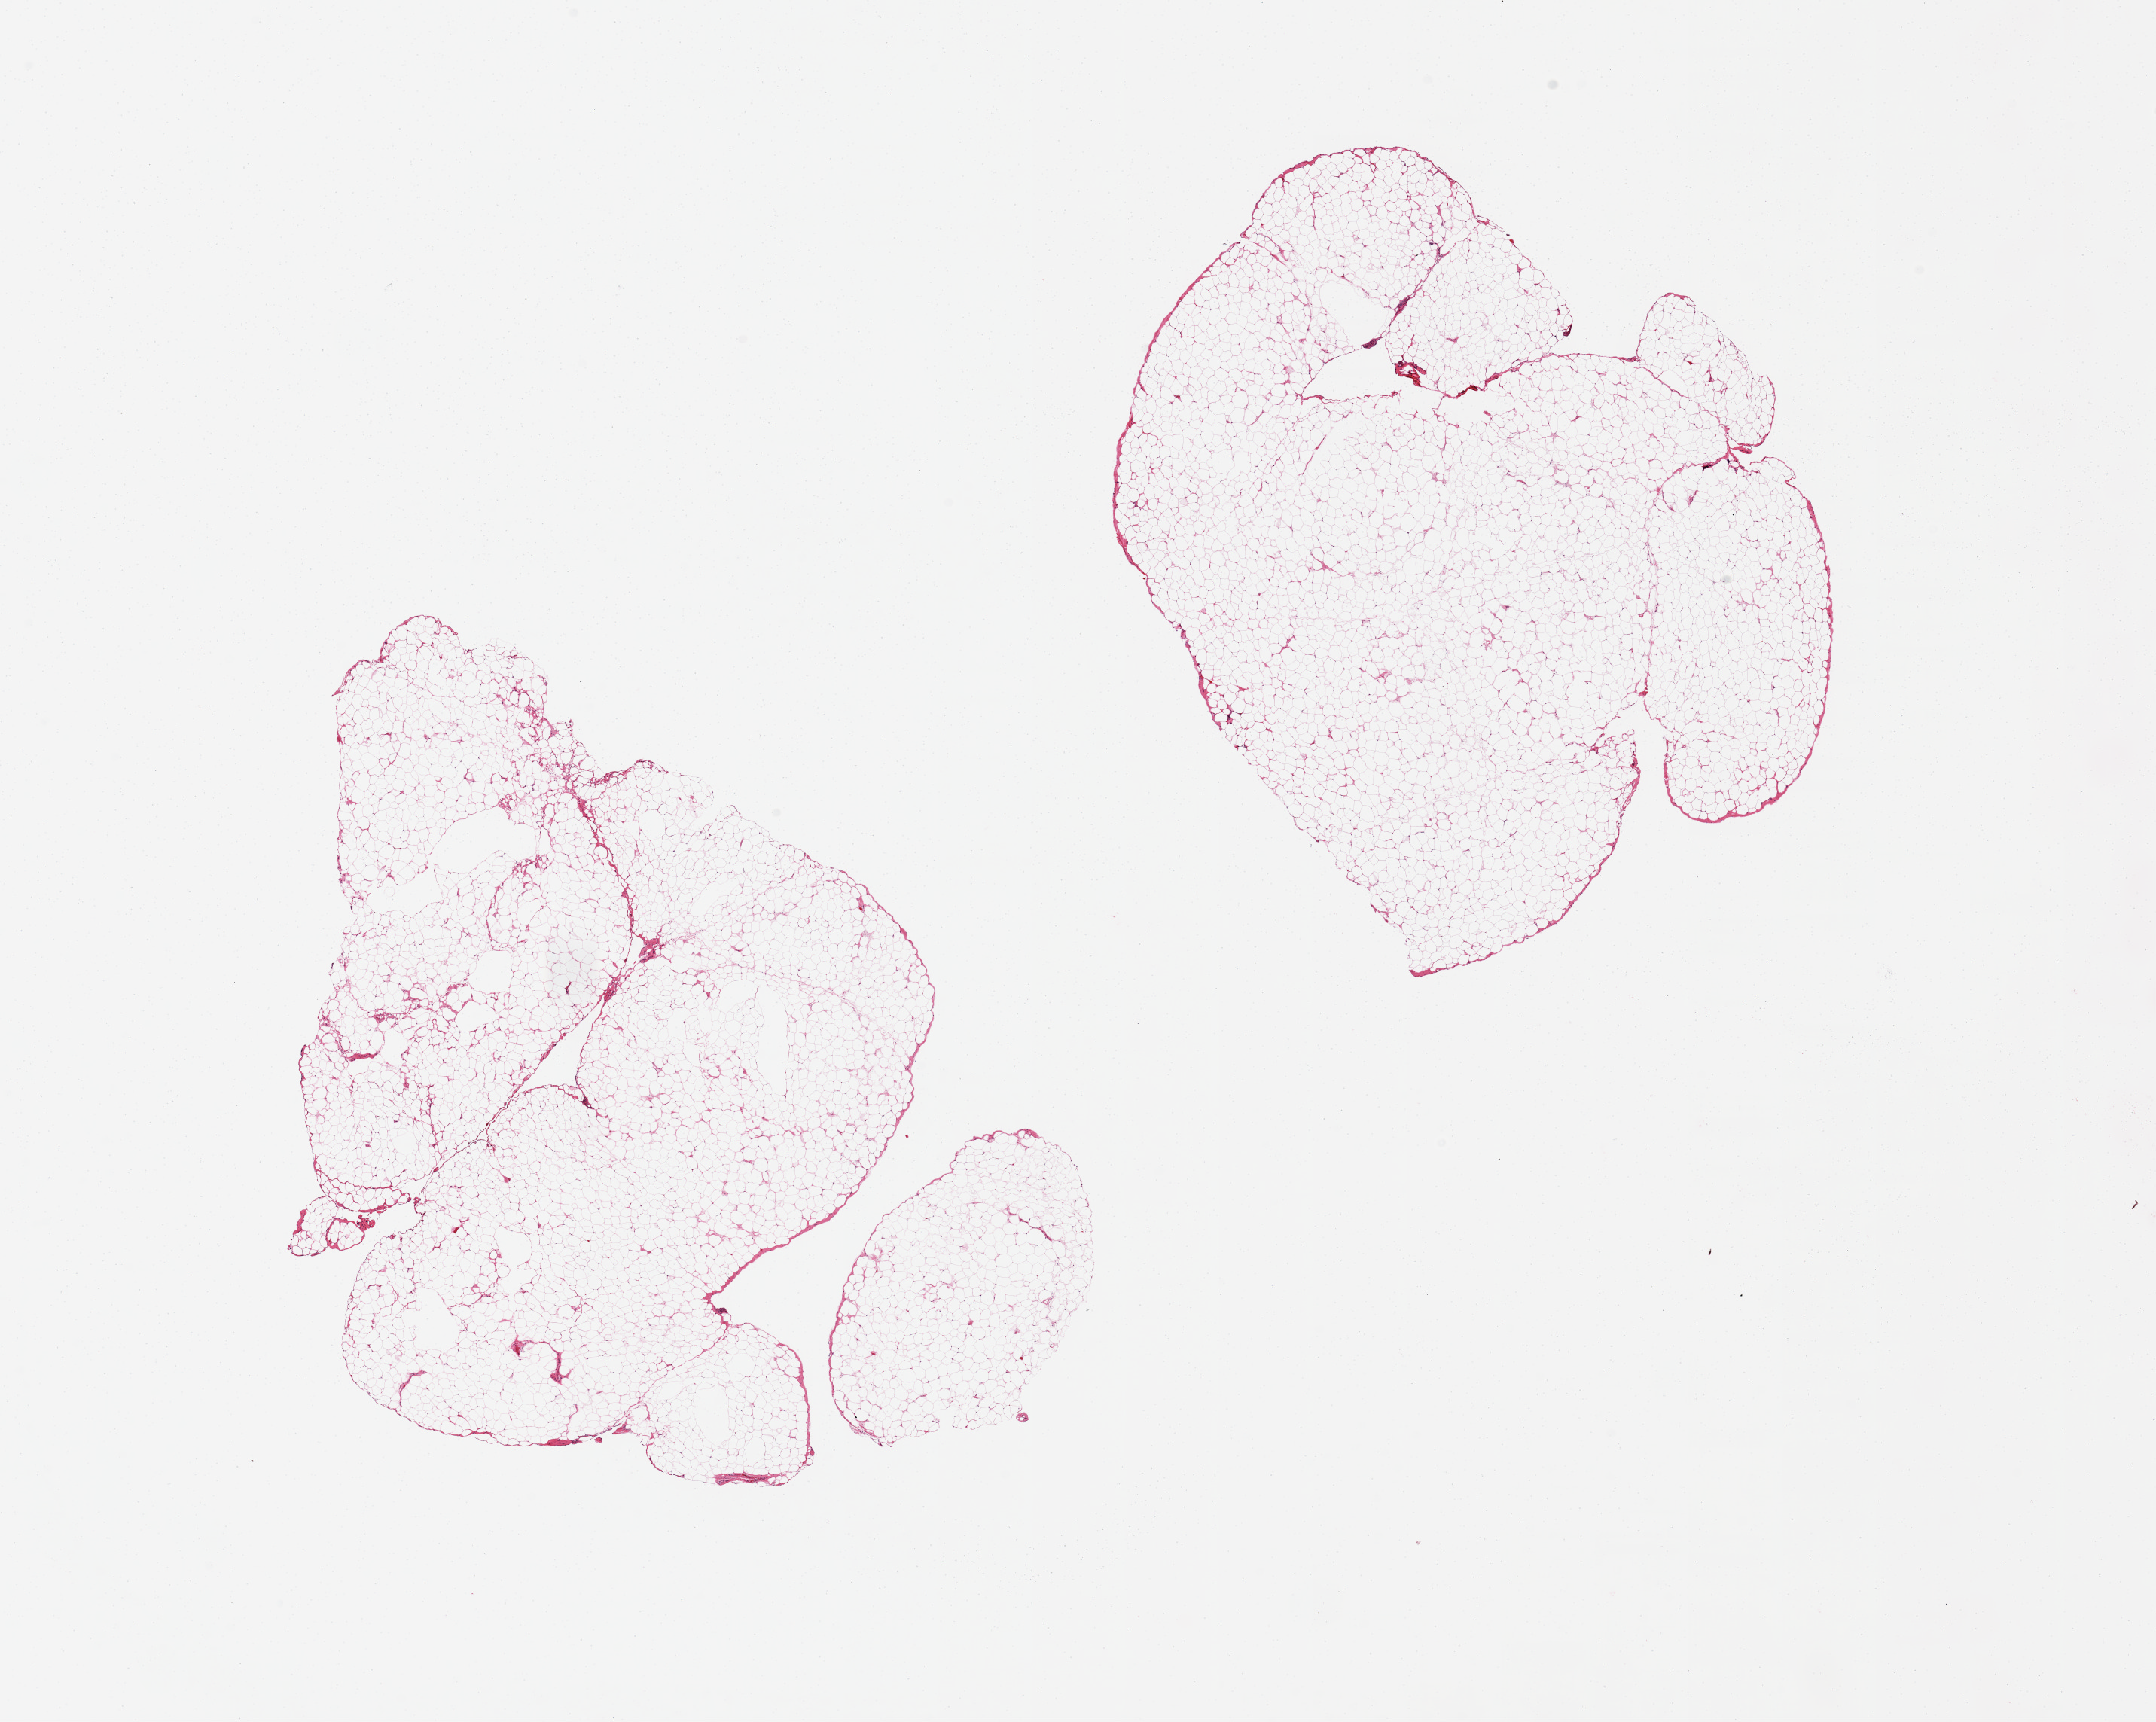
Whole-slide image, haematoxylin and eosin stain, brightfield, low-resolution overview of the scanned area, about 22.6 x 18.1 mm (acquisition: 20x scan). PAXgene-fixed paraffin-embedded (PFPE) section. Sampled site (target tissue): omentum. Tissue donor sample. Donor sex: male.
Review note (as recorded): 2 pieces, trace fascia.